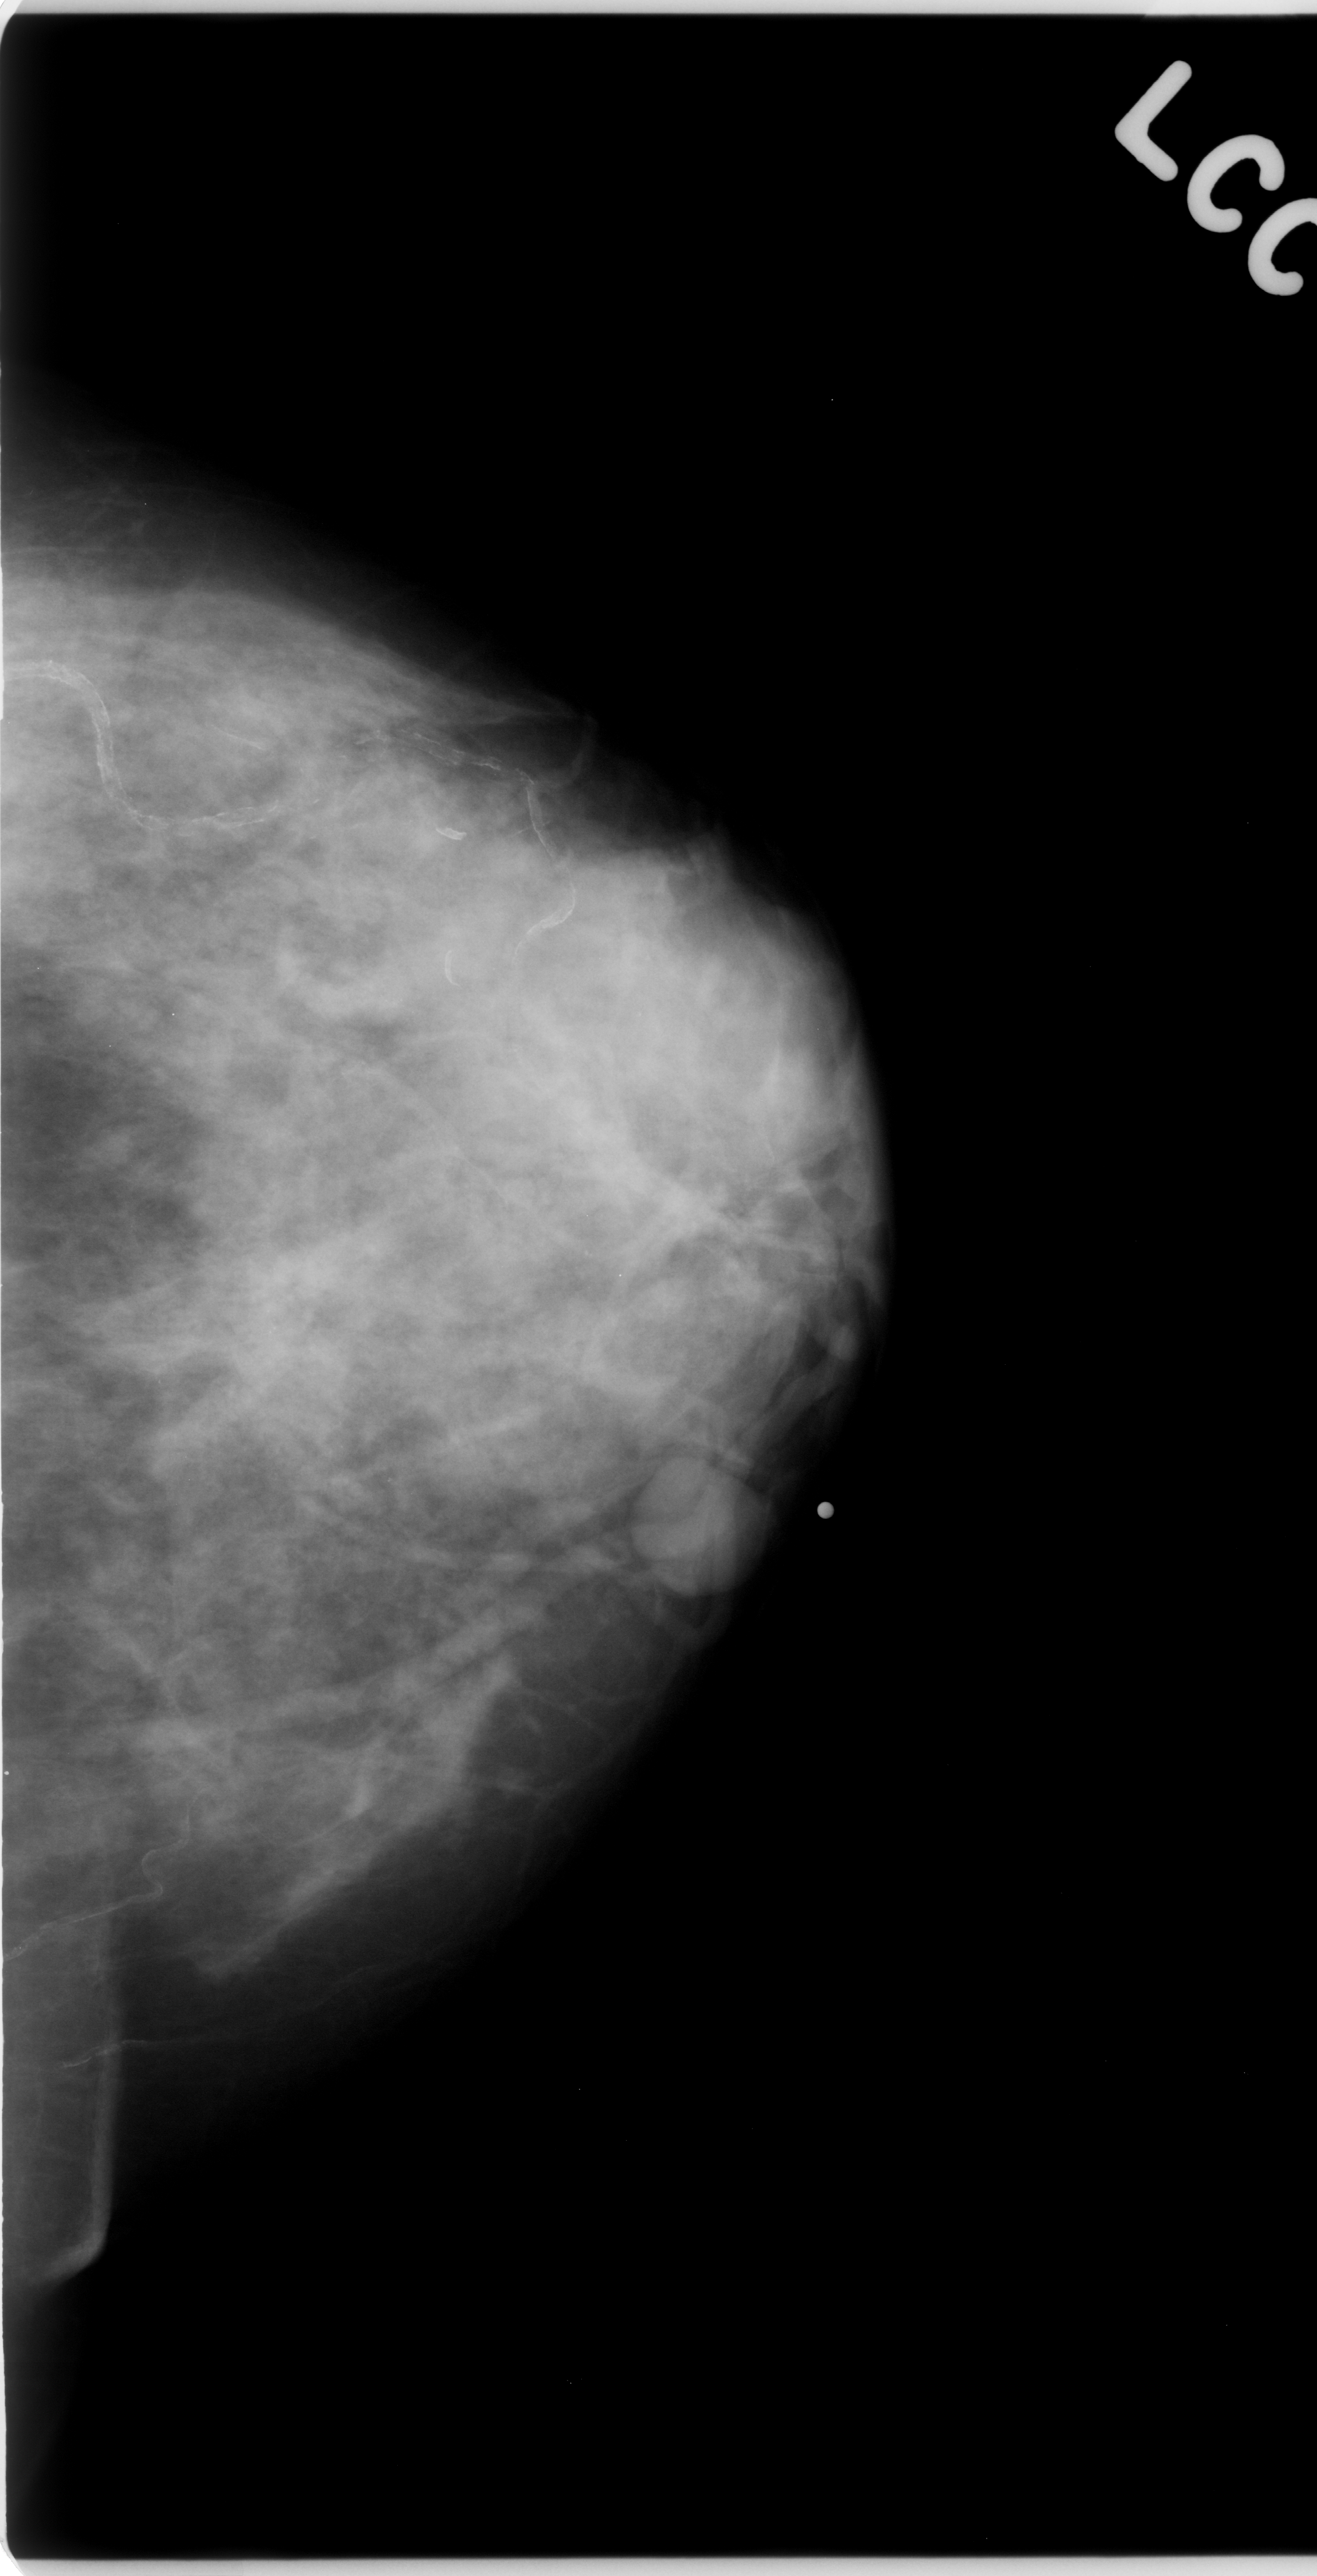
Digitized screen-film mammogram. Left breast. CC view. Breast composition: heterogeneously dense (BI-RADS density category 3 of 4). 1317 × 2576 image matrix.
Expert-marked regions of interest on this film, with their recorded descriptors:
- mass, shape oval, margins circumscribed; BI-RADS assessment category 3; pathology (as recorded): benign: bounding box <633,1460,768,1597> (left, top, right, bottom; pixels)